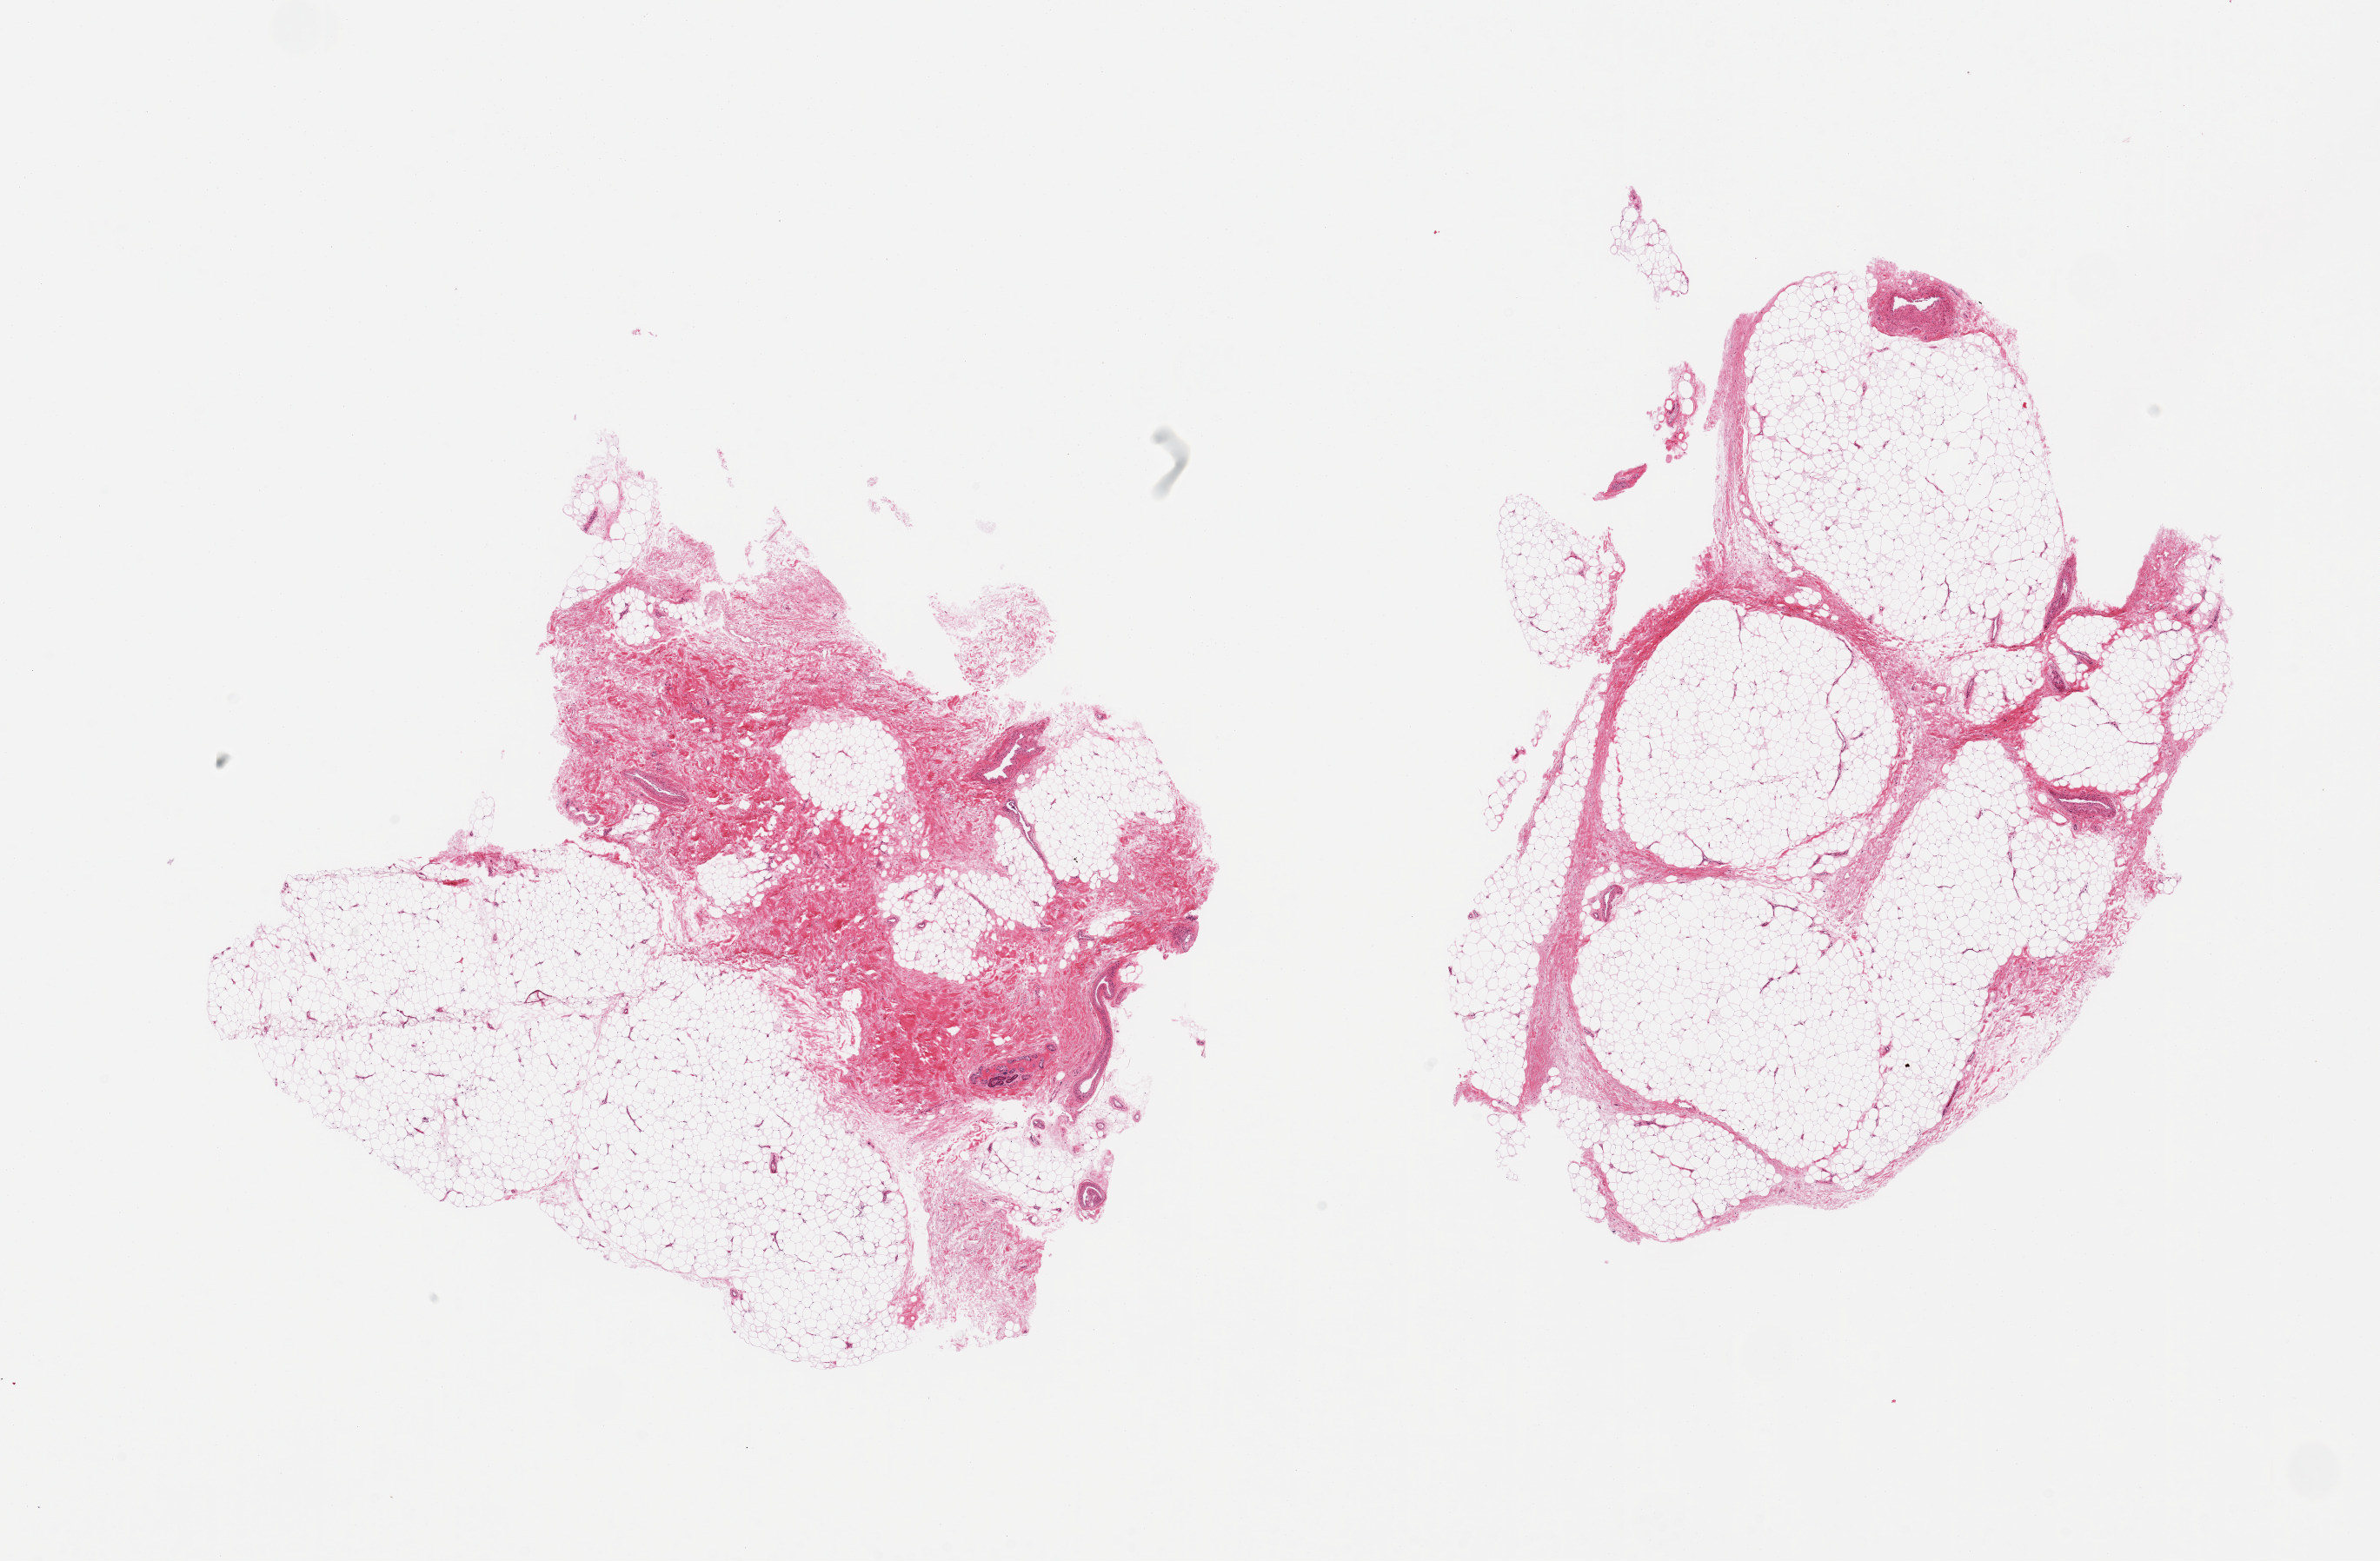
Whole-slide image, haematoxylin and eosin stain — whole scanned area (about 21.7 x 14.2 mm) shown as a low-resolution overview; PAXgene-fixed paraffin-embedded (PFPE) section; section of adipose tissue (target tissue); donor tissue sample. Male donor.
Pathologist's review note for this sample: 2 pieces: 1 with 60% fibrous content & a focus of sweat glands.